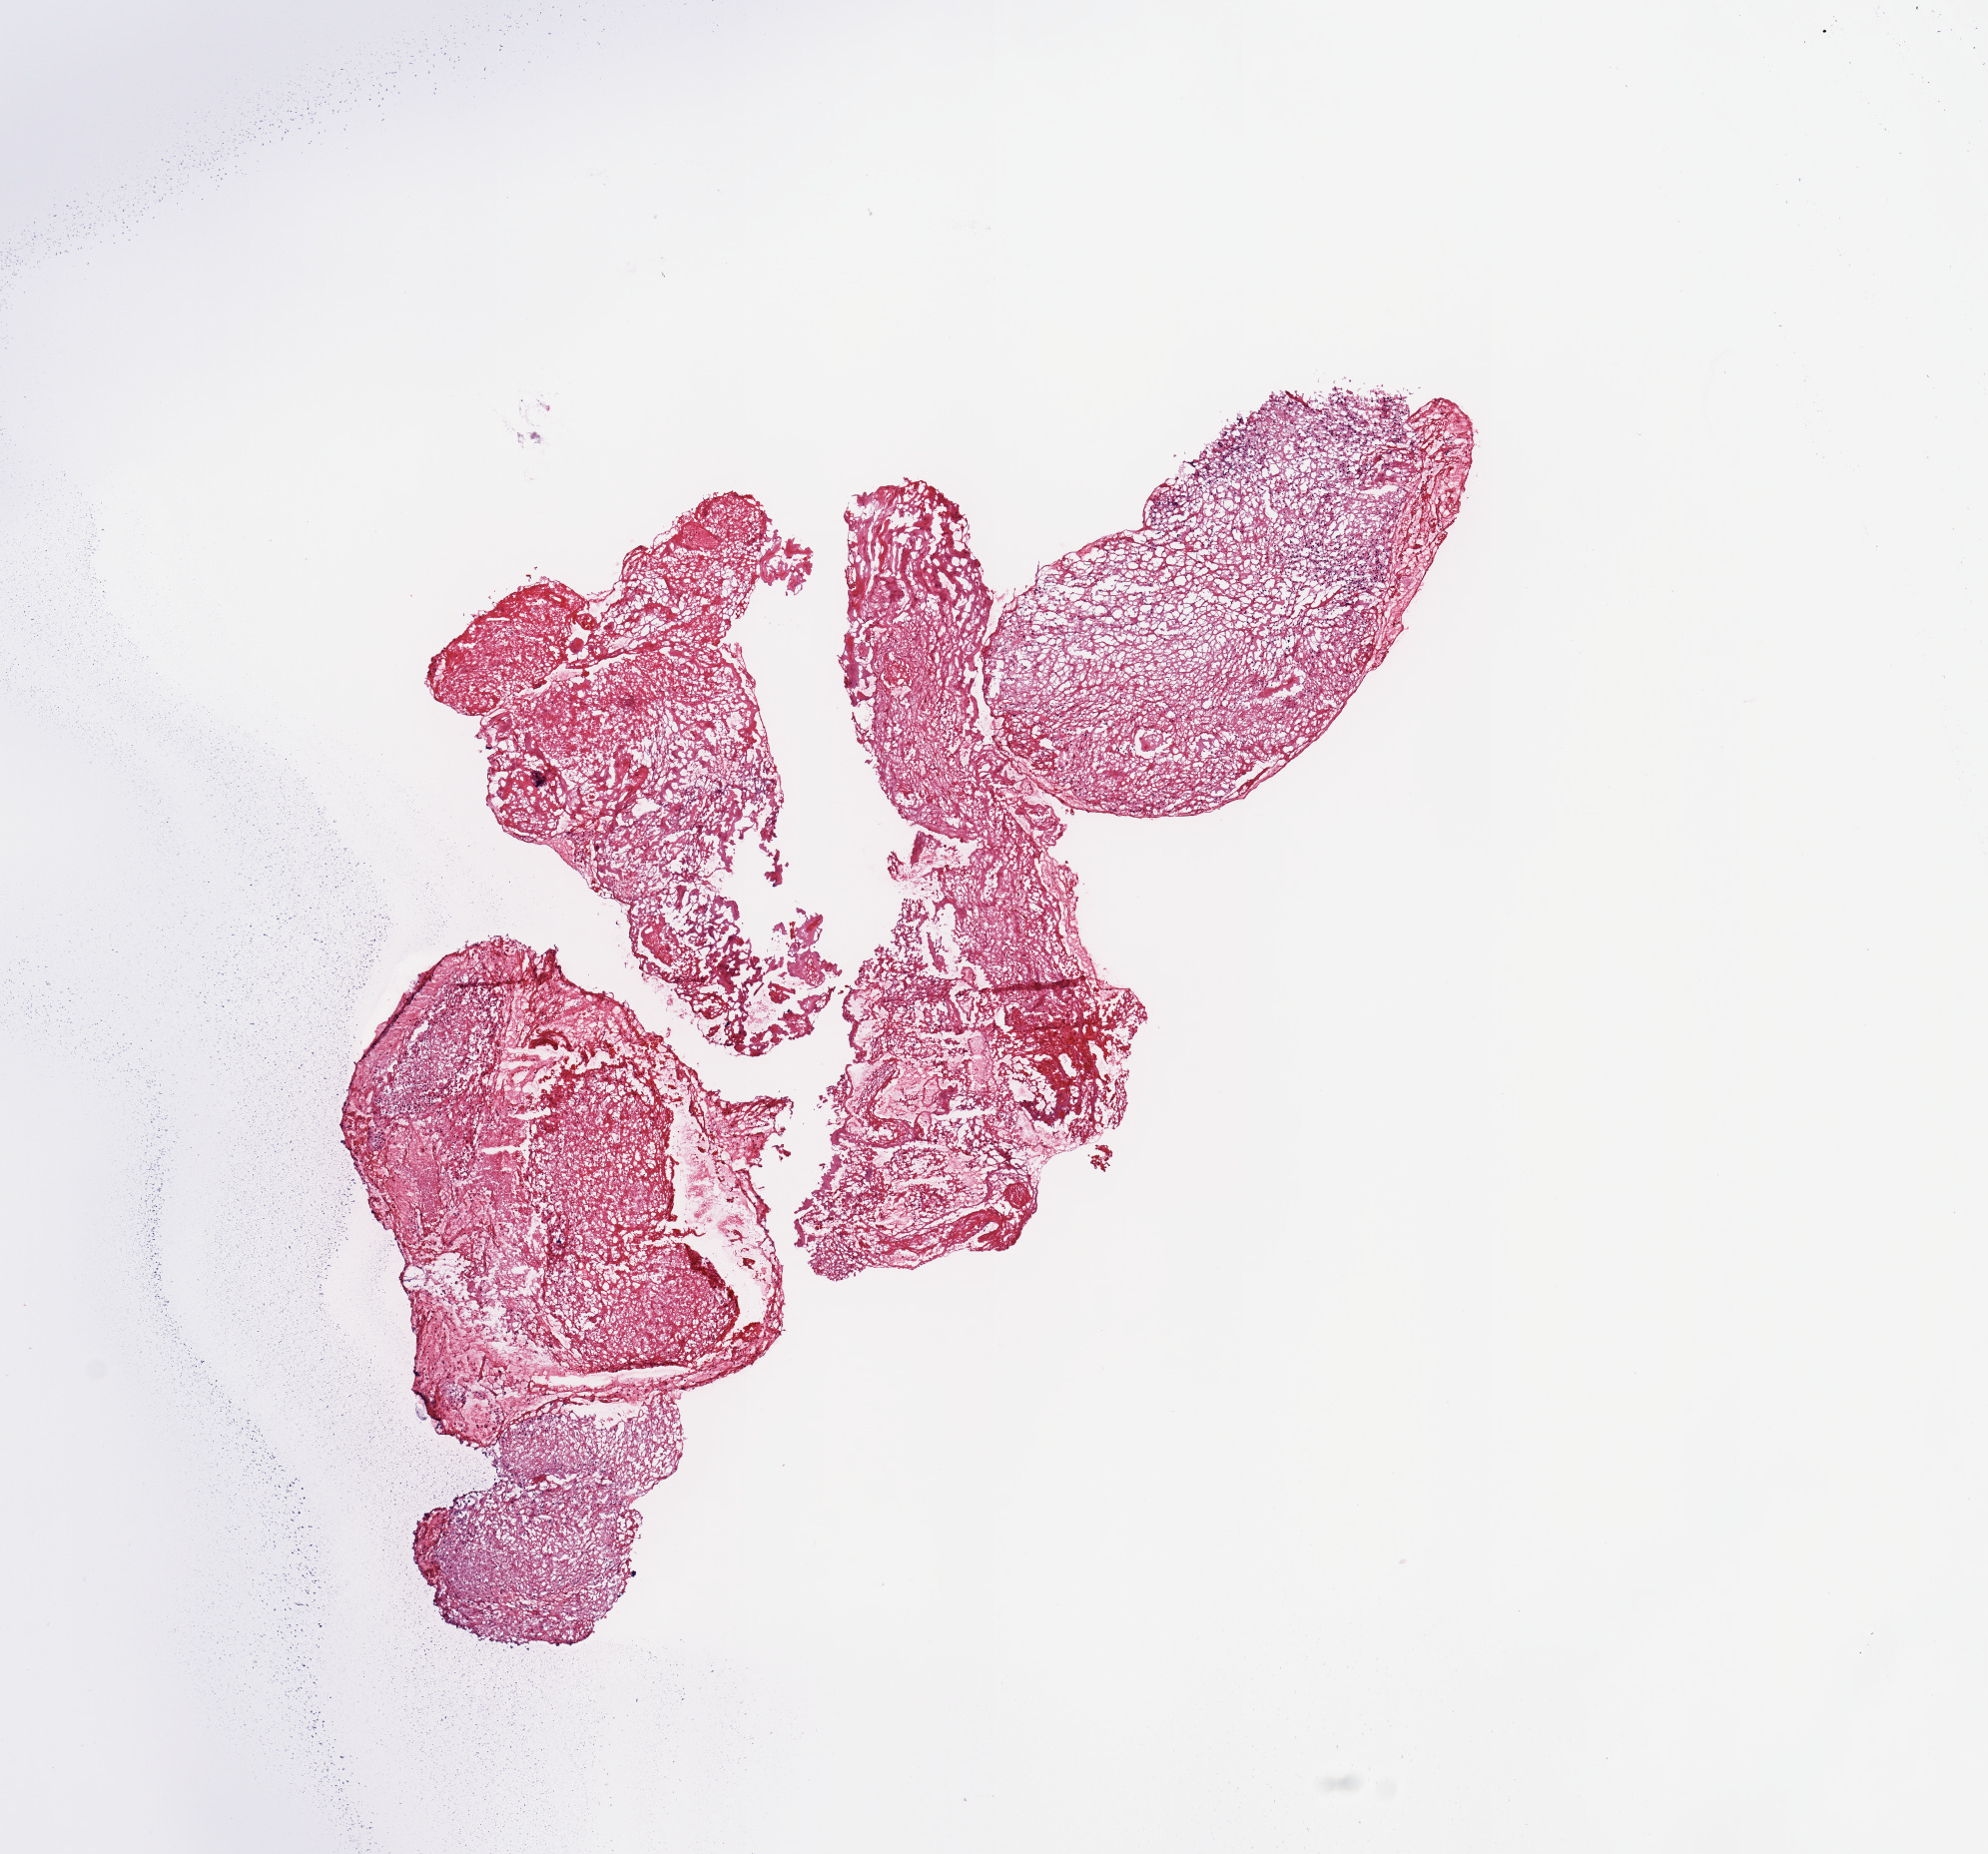
Digitized H&E-stained tissue section (whole slide), shown as a low-resolution overview of the whole scanned area (about 7.9 x 7.3 mm, acquisition: 20x scan), brain, tumour tissue. 61-year-old male patient.
• primary tumour site (as recorded): frontal lobe
• patient diagnosis (cohort enrolment): glioblastoma multiforme (brain)